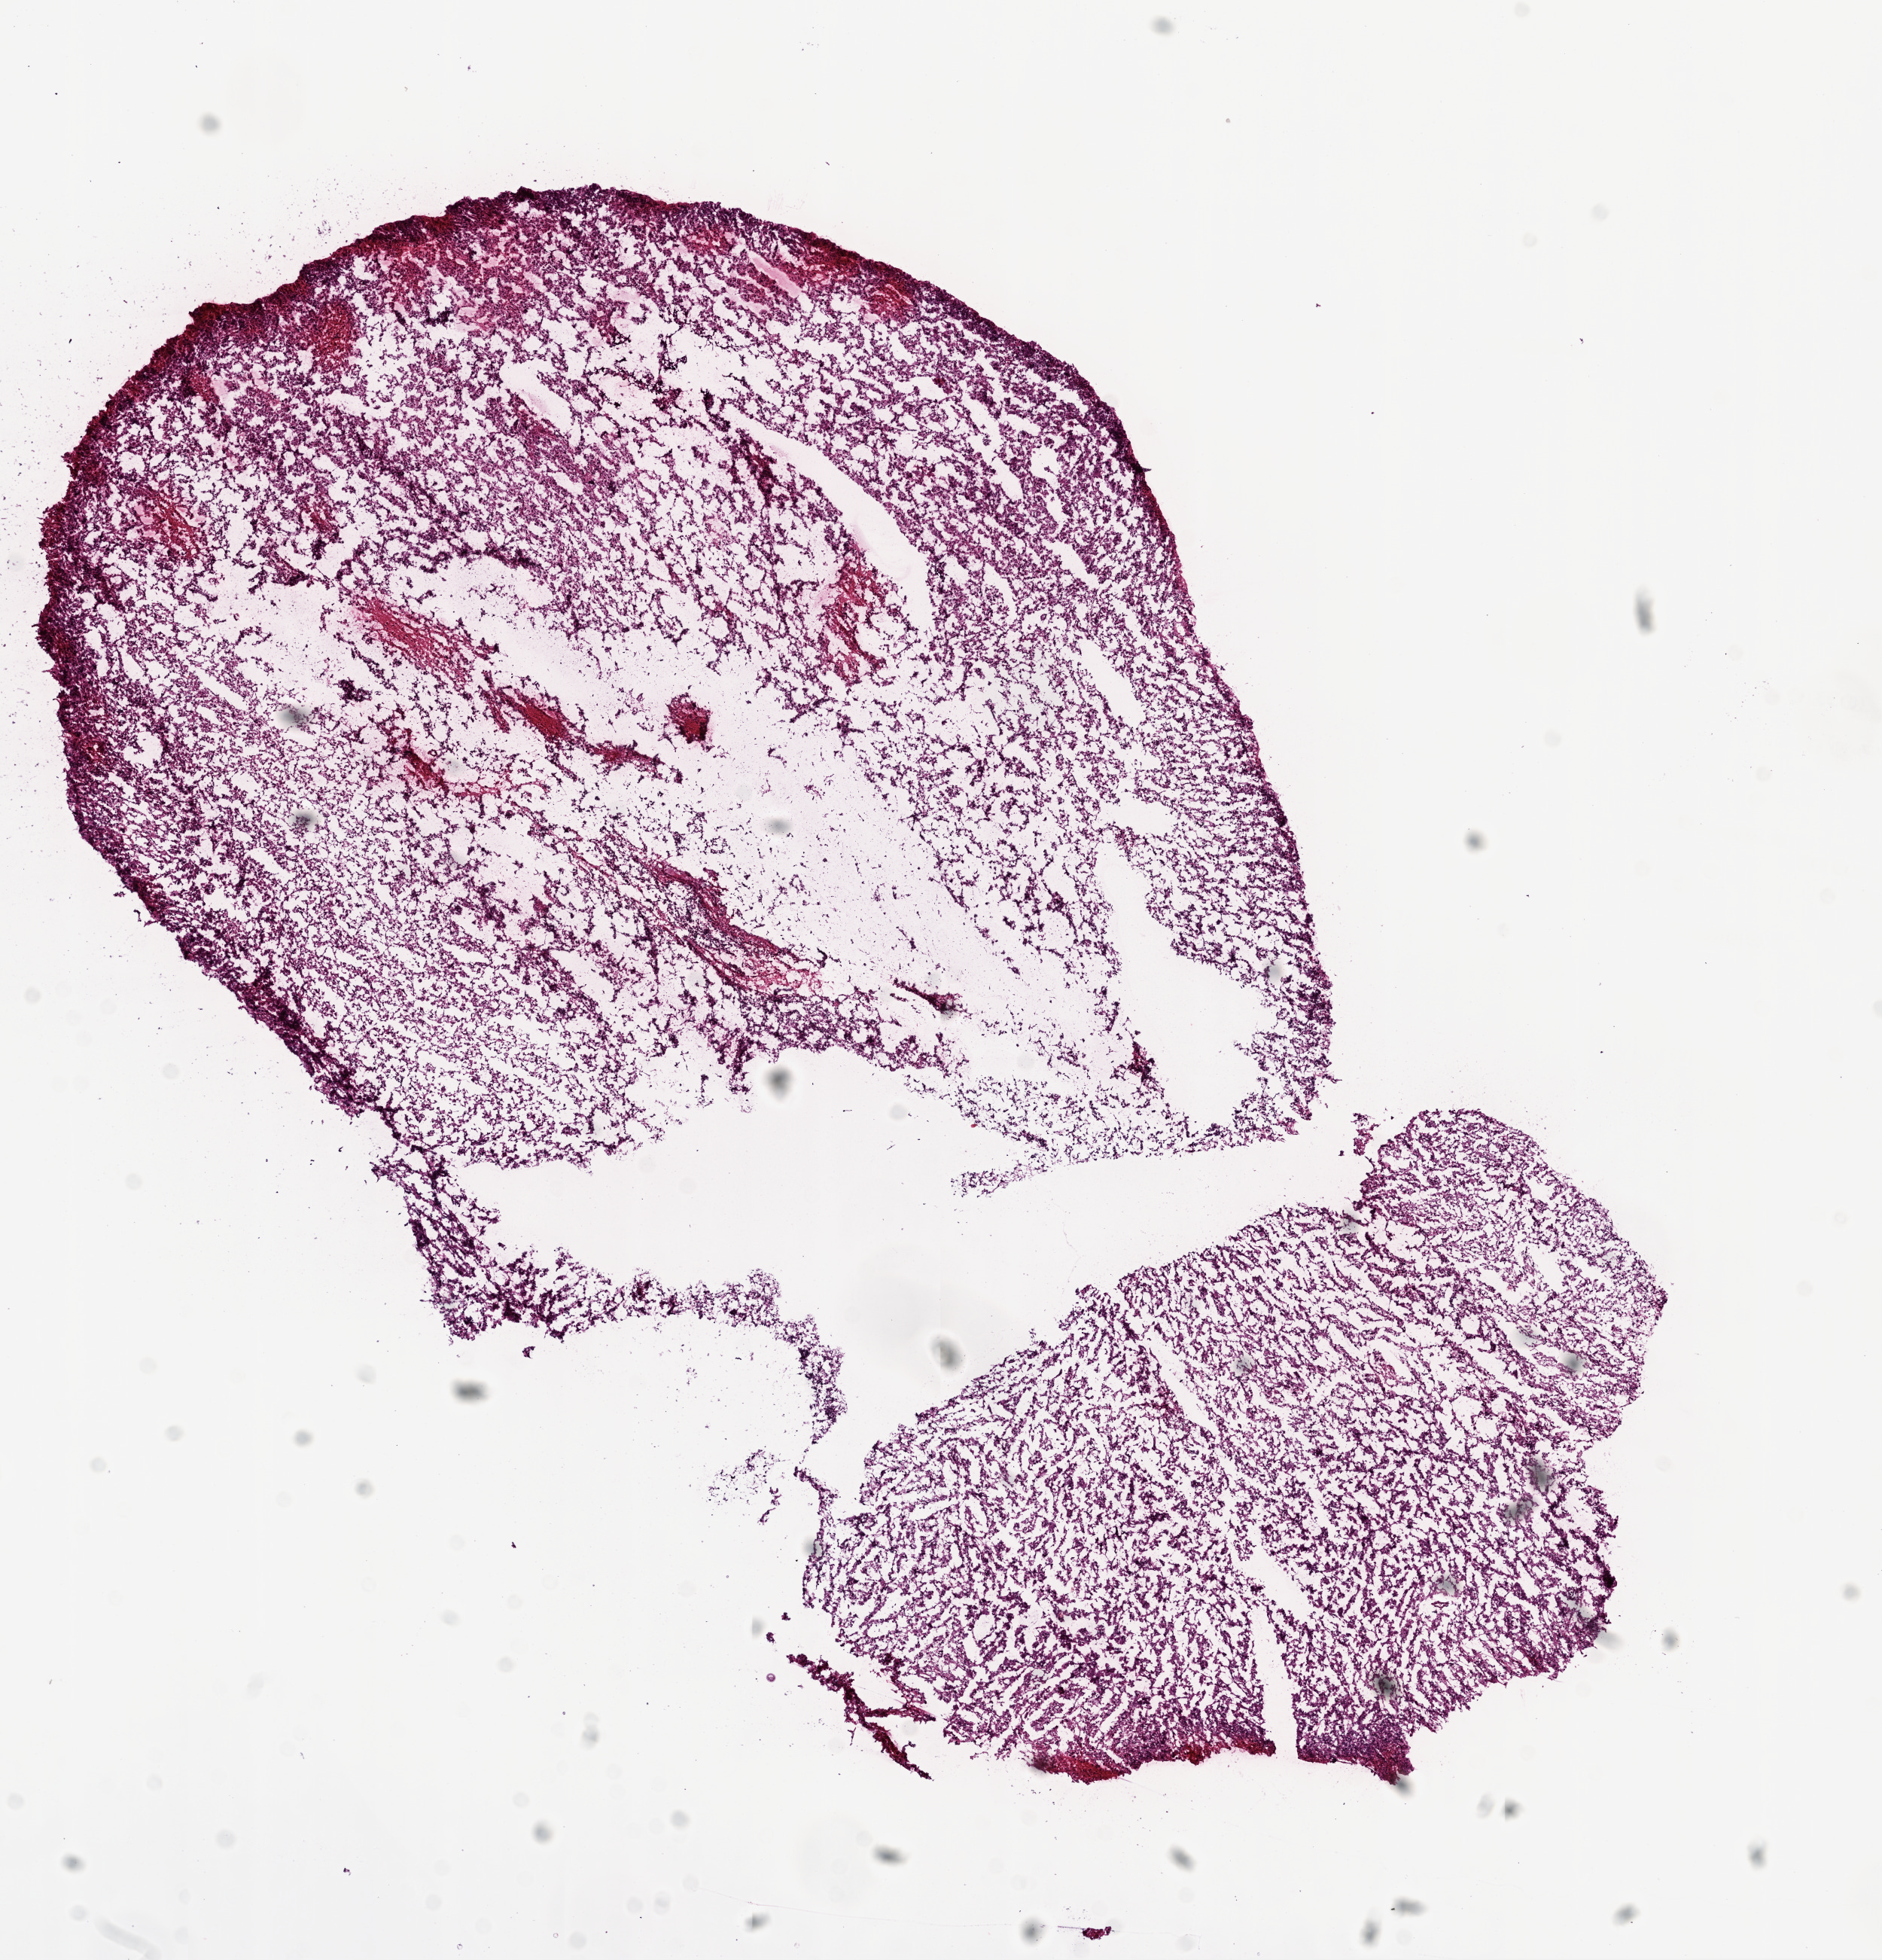
Digitized H&E tissue section (whole slide), a low-resolution overview of the entire scanned area, about 10.0 x 10.4 mm; frozen section from the top of the tissue portion; sample: primary tumour, brain. Male patient; age at initial diagnosis 31 years. Histologic grade: G3 (poorly differentiated). Slide review estimates, as recorded: tumour cells 100%, tumour nuclei 75%, normal cells 0%, stromal cells 0%, necrosis 0%.
Laterality: right. Histologic diagnosis: Oligodendroglioma, anaplastic.